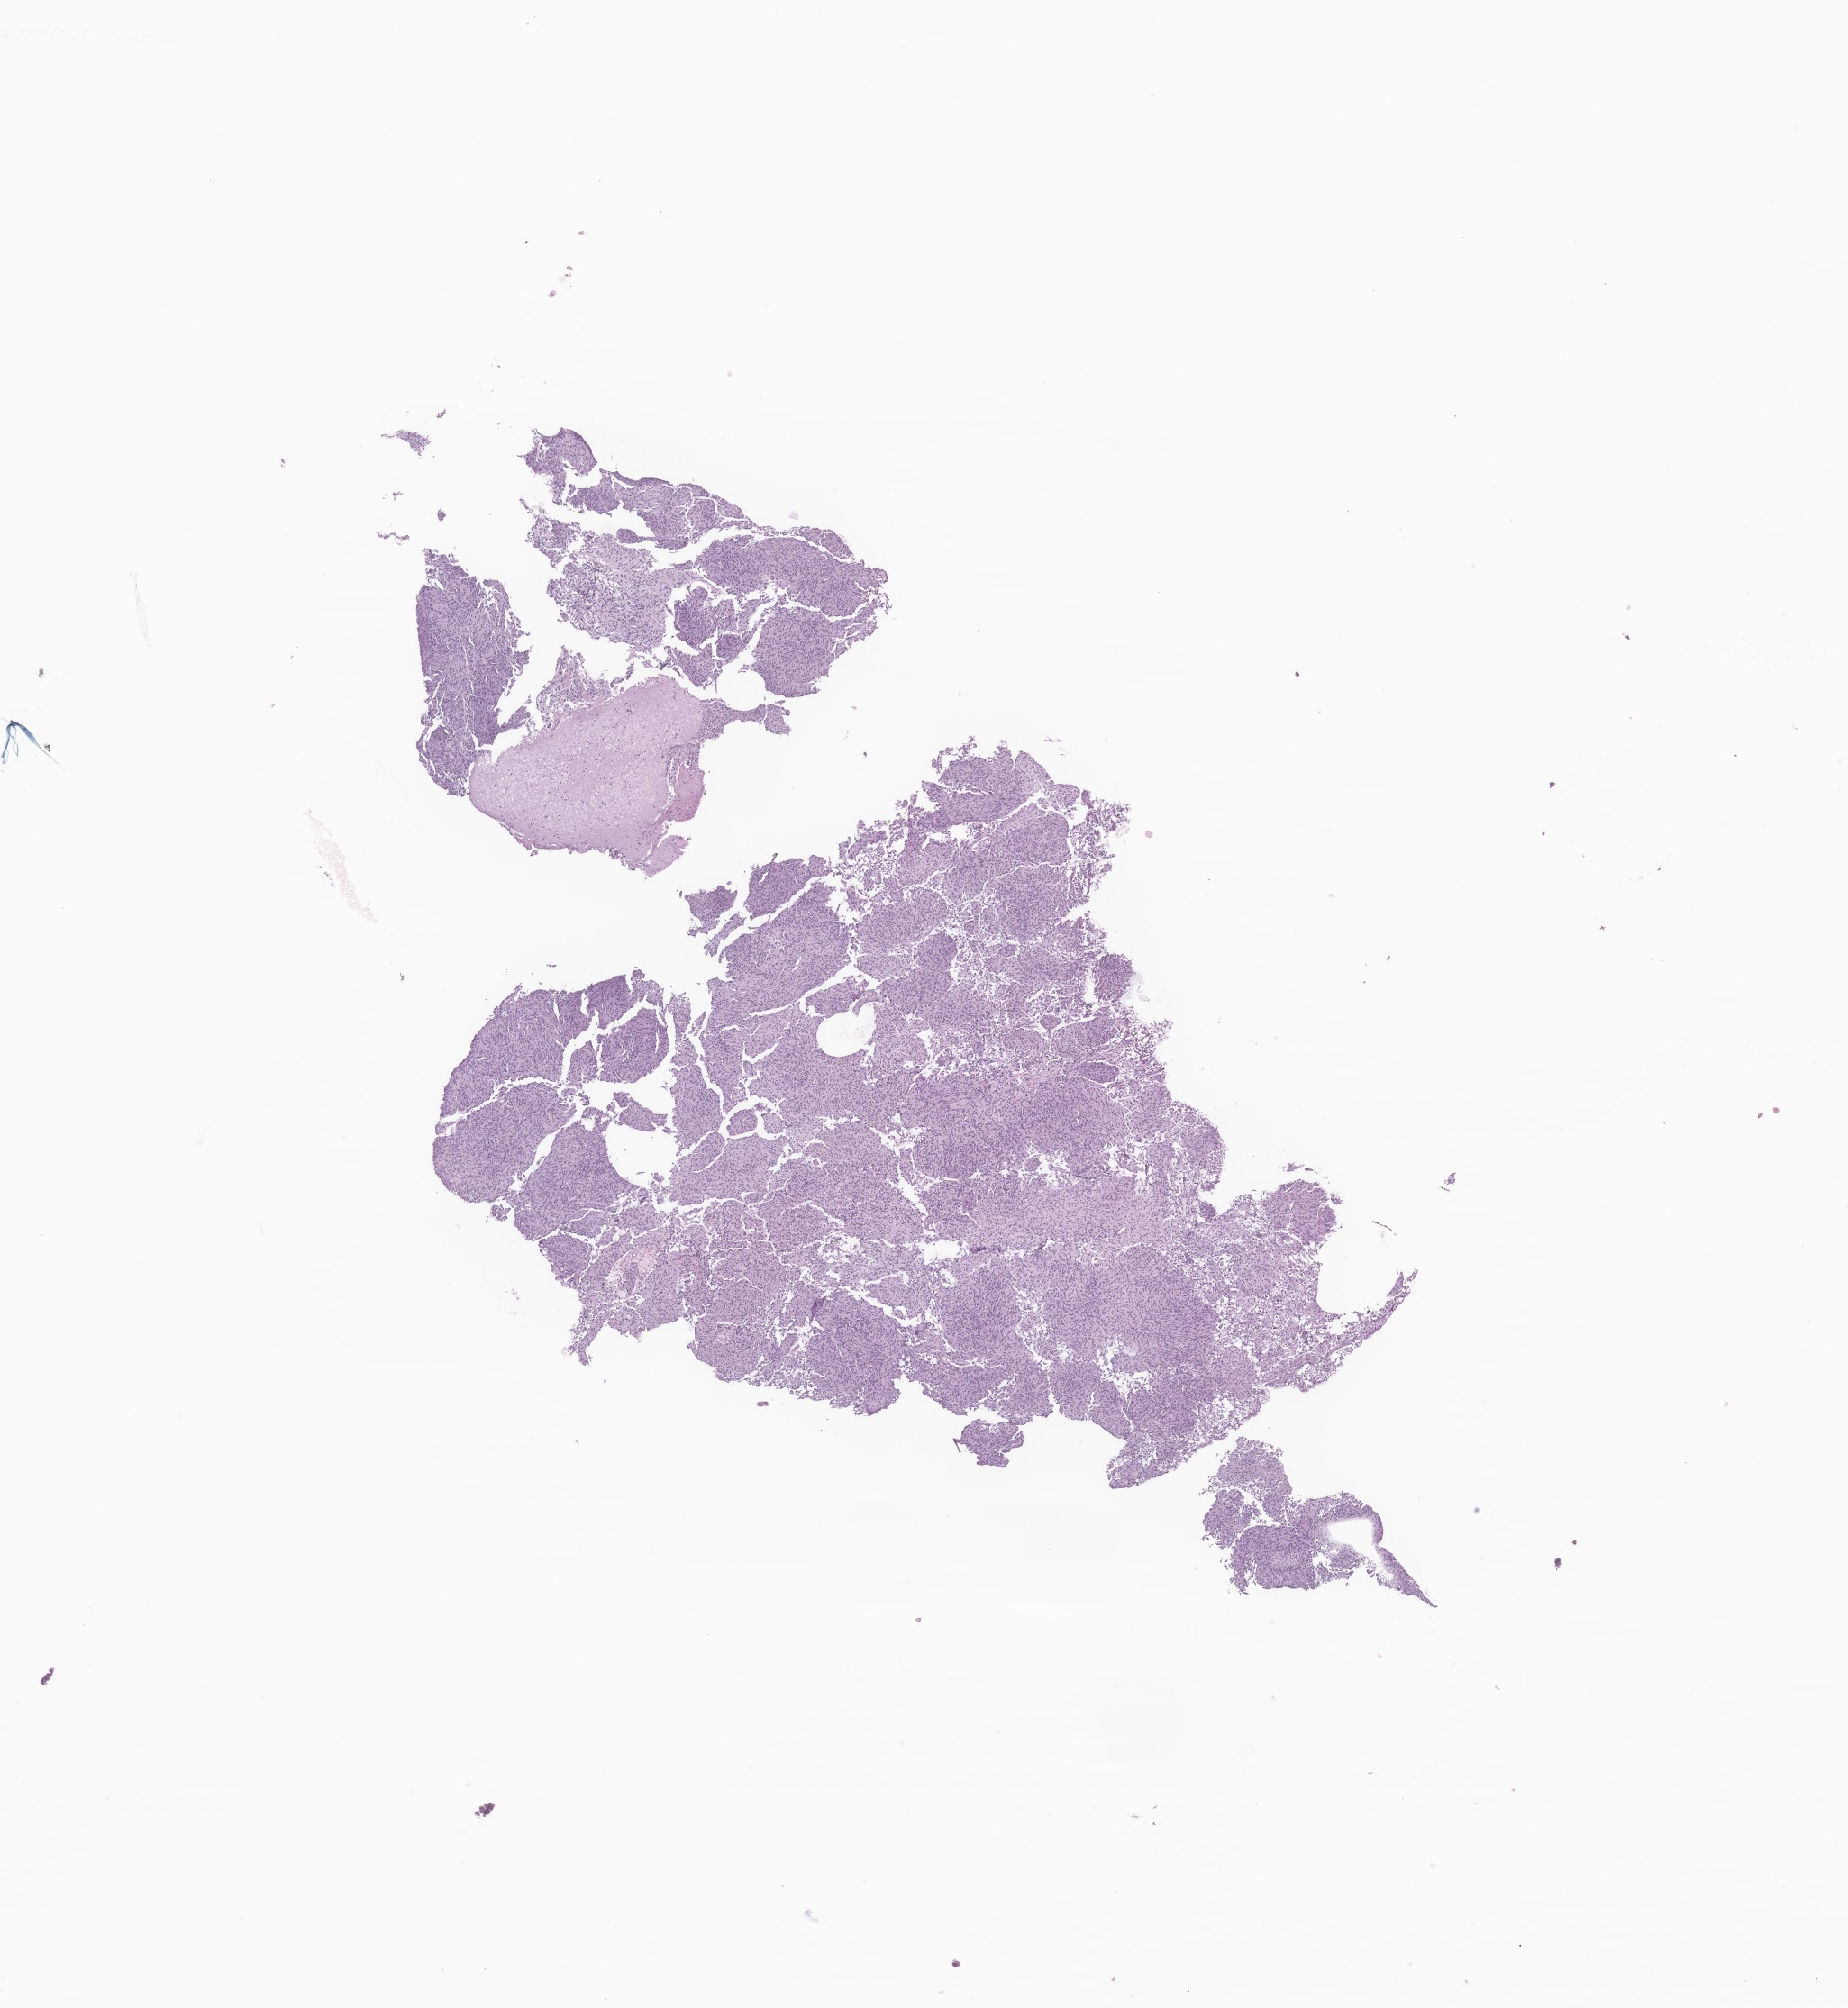
Digitized hematoxylin and eosin (H&E)-stained section of tumor tissue from the brain — shown as a low-resolution overview of the whole scanned area (about 8.6 x 9.4 mm), FFPE section. Patient: female, age 229 months (19 years 1 month).
Diagnosis (ICD-O-3 morphology term): Meningioma, NOS.